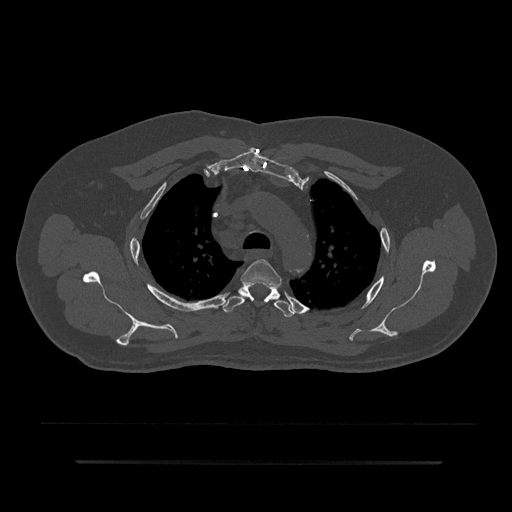
CT including the spine, one axial slice. Position 637 of 797 along the scan axis. Reconstruction kernel Br40s/3. Bone window (W 1800 / L 400 HU). 512 × 512 image matrix, field of view 464 × 464 mm. Patient: male, 59 years. From the clinical record (not read from this slice): primary cancer: bile ducts; vertebrae with lytic lesions (as recorded): T10.
Outlined on this slice (semi-automatic segmentation, software-assisted and operator-edited):
- T3 vertebra: bounding box <240,259,282,288> (left, top, right, bottom; pixels)
- T4 vertebra: <222,284,294,317>